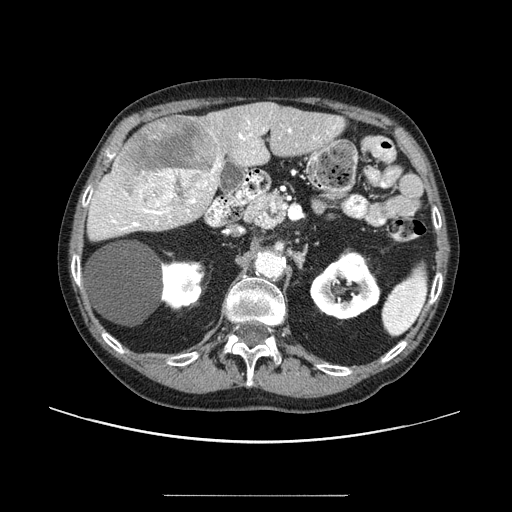
Contrast-enhanced abdominal CT (liver protocol), one axial slice; slice 46 of 91 in the series (ordered by position); reconstruction kernel STANDARD; one of 2 acquisitions stored at this slice position; soft-tissue window (W 400 / L 40 HU); 512 × 512 image matrix, field of view 400 × 400 mm. Case-level facts recorded for this patient, not image findings: diagnosis: hepatocellular carcinoma (patient treated with transarterial chemoembolisation; whether this scan precedes or follows treatment is not stated here); TNM stage (as recorded): Stage-I; Child-Pugh class: A; tumour differentiation: moderately differentiated.
Outlined on this slice (semi-automatically segmented with operator editing):
- liver parenchyma outside the tumour (the mass and vessels are separate outlines, so this box may not span the whole liver): bounding box (x1, y1, x2, y2) in pixels: (90, 102, 344, 234)
- mass: (113, 115, 220, 213)
- liver vessels: (103, 121, 335, 230)